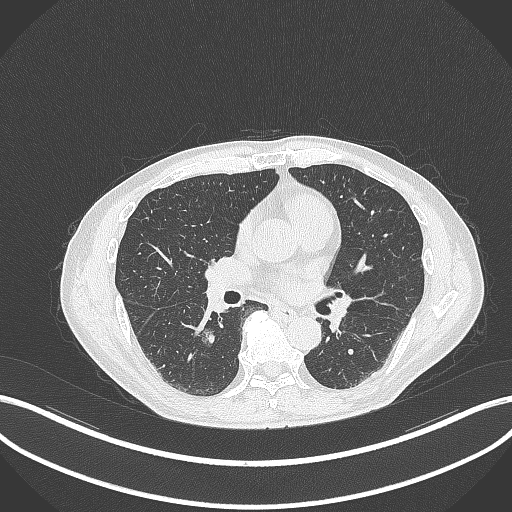
Chest CT, one axial slice. Slice 163 of 323 in the series (ordered by position). Reconstruction kernel B70f. Lung window (W 1500 / L -600 HU). 512 × 512 image matrix. Male patient, age 61 years. From the clinical record (not read from this slice): clinical TNM (as recorded): T1c N0 M0.
Outlined on this slice (bounding box drawn by a radiologist):
- lung tumour (recorded histology: adenocarcinoma): bounding box <198,328,218,350> (left, top, right, bottom; pixels)